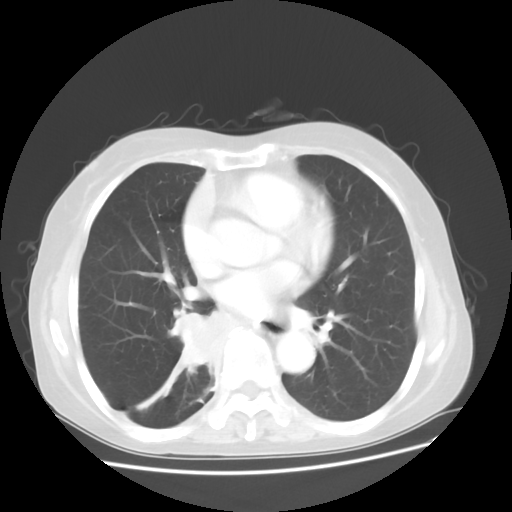
Chest CT, one axial slice; lung window (W 1500 / L -600 HU); 5 mm slice thickness; 512 × 512 image matrix, field of view 360 × 360 mm. Patient: female, 63 years. From the clinical record (not read from this slice): clinical TNM (as recorded): T2 N3 M1b; histopathological grade: G3.
Structures marked on this image (bounding box drawn by a radiologist):
- lung tumour (recorded histology: small cell carcinoma): bounding box <175,312,222,377> (left, top, right, bottom; pixels)